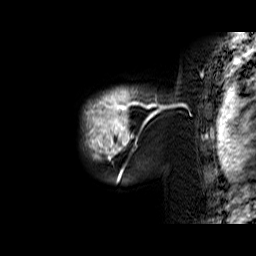
Breast MRI (dynamic contrast-enhanced), one sagittal slice; position 54 of 60 along the scan axis; dynamic contrast-enhanced series, time point 2 of 6 at this slice position (early post-contrast); 1.5 T; TE 6.4 ms, TR 32.9 ms; 4 mm slice thickness; 256 × 256 image matrix. Female patient. Case-level facts recorded for this patient, not image findings: setting: breast cancer imaged before/during neoadjuvant chemotherapy; receptor status: triple-negative.
Structures marked on this image (semi-automatic segmentation, software-assisted and operator-edited):
- analysis volume of interest (the breast-tissue region the enhancement analysis was run in; not a lesion): box from (x=84, y=87) to (x=159, y=174) px
- tumour enhancement mask (voxels above the 100 % enhancement threshold inside the analysis volume of interest): (x=85, y=87)–(x=159, y=174)